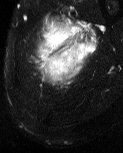
MRI of an extremity soft-tissue mass, one axial slice; position 13 of 60 along the scan axis; T2-weighted fat-saturated; MR volume resampled by the dataset authors to the PET/CT grid (not the native acquisition matrix); 3.27 mm slice thickness; 123 × 153 image matrix, field of view 120 × 149 mm. Male patient. From the clinical record (not read from this slice): histological type: pleiomorphic liposarcoma; grade: high; site of the primary tumour: left thigh.
Structures marked on this image (expert contour drawn on MRI and transferred to this co-registered scan by the dataset authors):
- gross tumour volume including surrounding oedema: bounding box <36,15,98,85> (left, top, right, bottom; pixels)
- gross tumour volume (mass): <57,65,62,67>